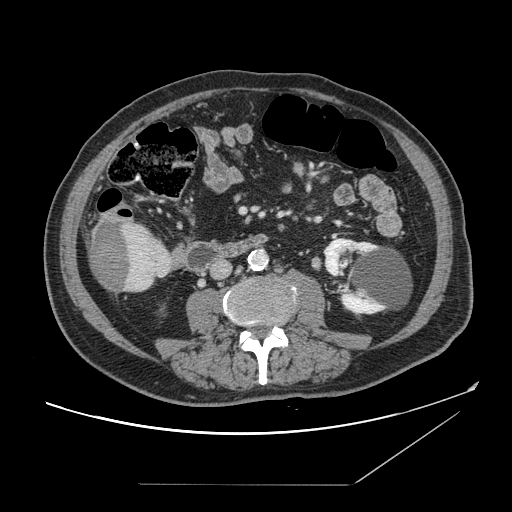
Contrast-enhanced abdominal CT, one axial slice. Position 35 of 166 along the scan axis. 120 kVp. Intravenous contrast given. Soft-tissue window (W 400 / L 40 HU). 2.5 mm slice thickness. 512 × 512 image matrix. Male patient, age 80 years. From the clinical record (not read from this slice): diagnosis: colorectal cancer liver metastases, imaged before liver resection; multiple liver metastases: no; largest metastasis: 2.2 cm; disease in both lobes: no.
Outlined on this slice (manually delineated by an expert):
- liver: box from (x=88, y=216) to (x=172, y=293) px
- liver metastasis: (x=92, y=221)–(x=132, y=290)